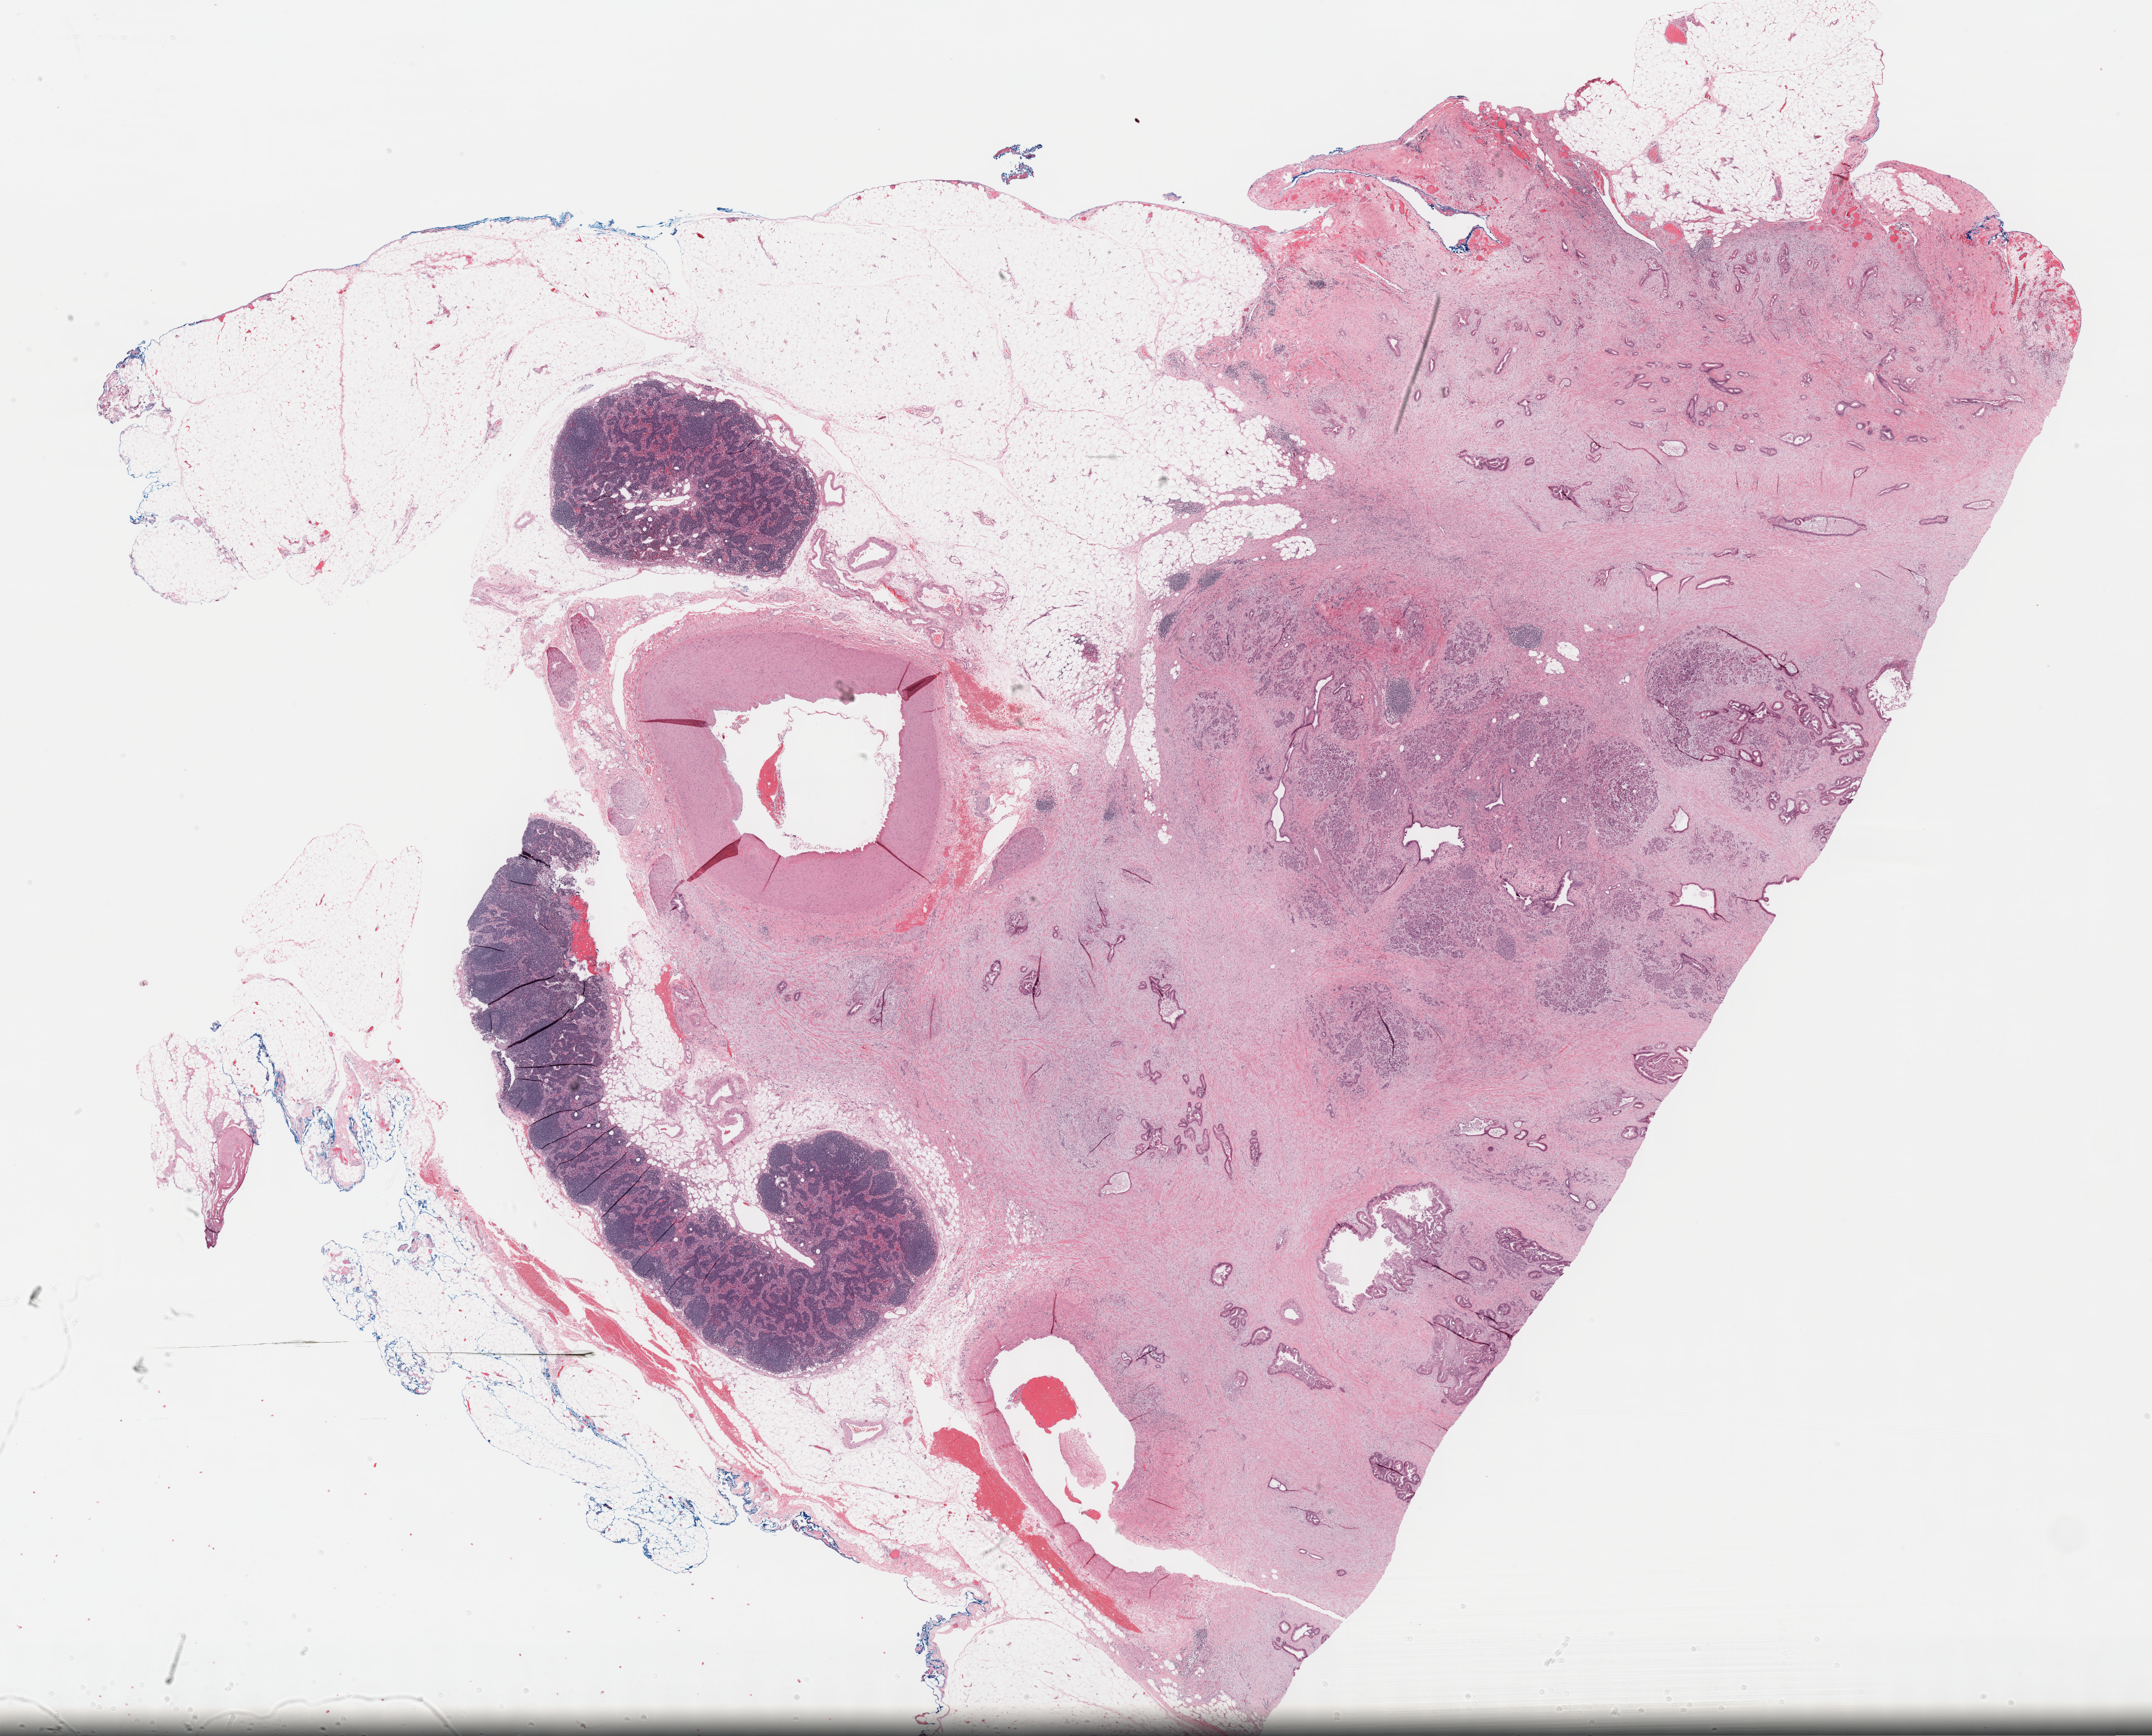
H&E whole-slide image, low-resolution overview of the scanned area, about 28.2 x 22.7 mm. Formalin-fixed paraffin-embedded (FFPE) diagnostic section. Sample: primary tumour, pancreas. Female, age 49 years at initial diagnosis. Histologic grade: G2 (moderately differentiated).
AJCC pathologic stage: IIB (7th edition). Diagnosis: Infiltrating duct carcinoma, NOS.